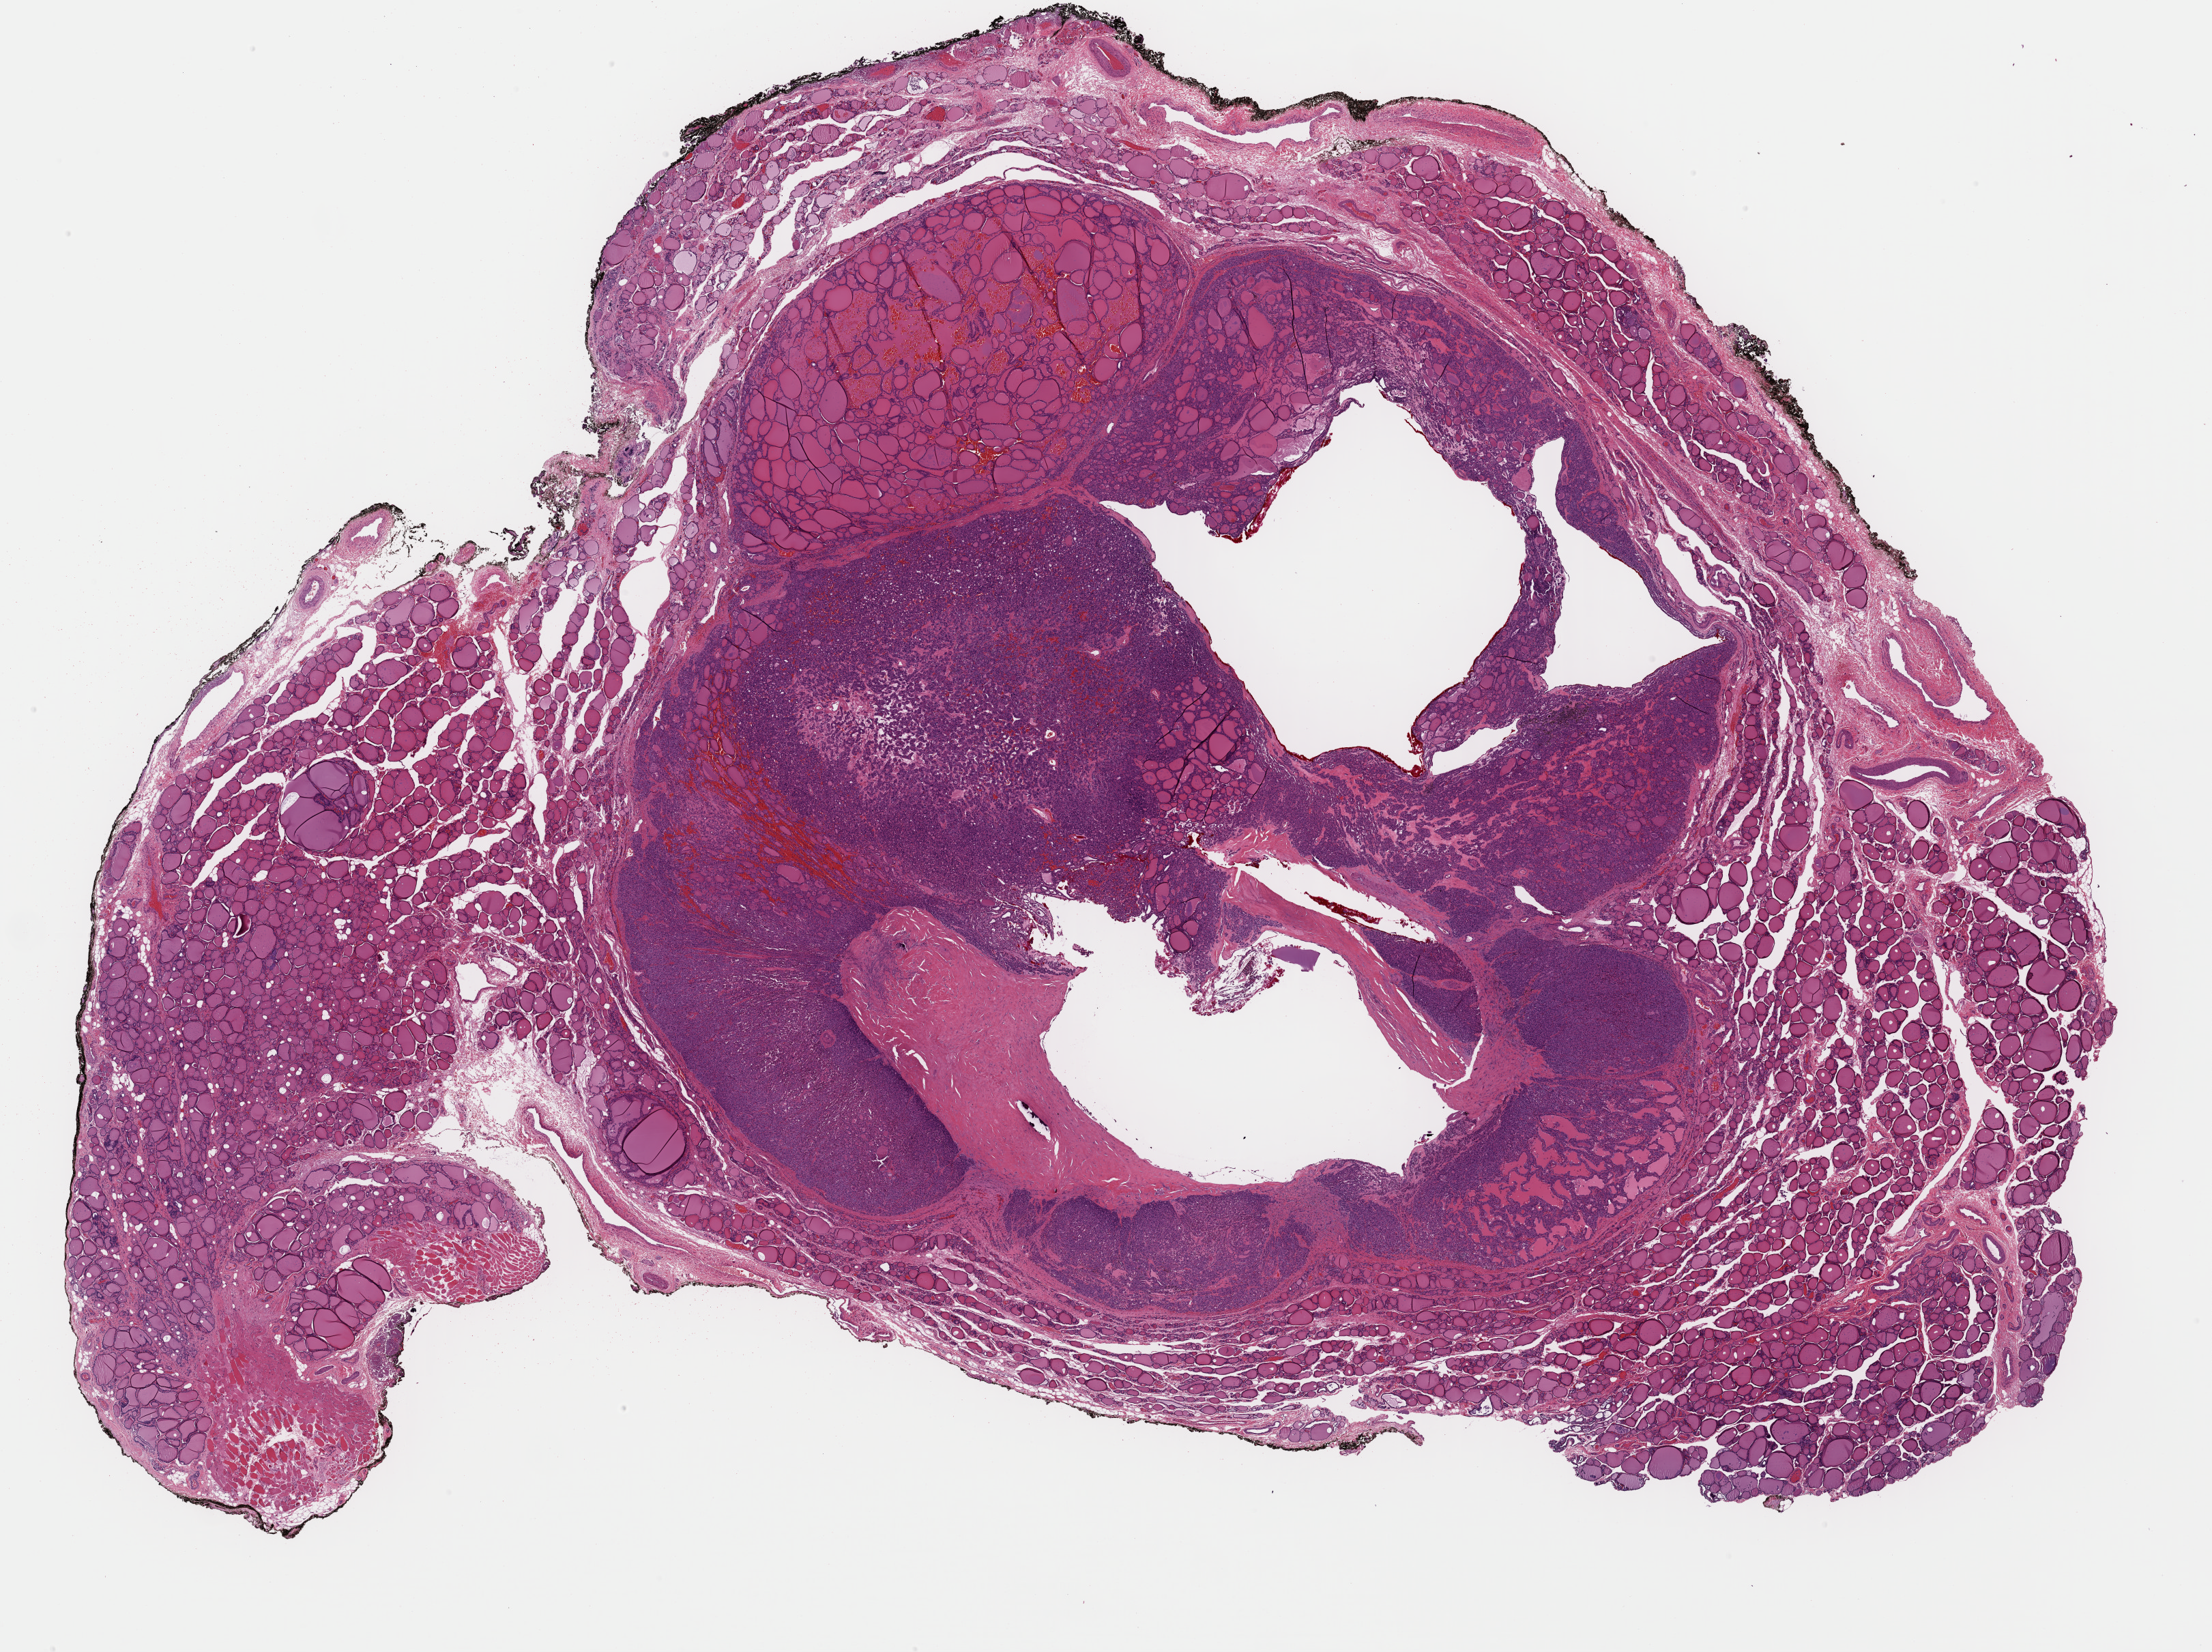
Digitized Hematoxylin and eosin (H&E) stained tissue section (whole slide), whole scanned area (about 25.6 x 19.1 mm) shown as a low-resolution overview; formalin-fixed paraffin-embedded (FFPE) diagnostic section; primary tumour sample from the thyroid. Female, age 59 years at initial diagnosis.
Pathologic diagnosis: Papillary adenocarcinoma, NOS (thyroid gland).